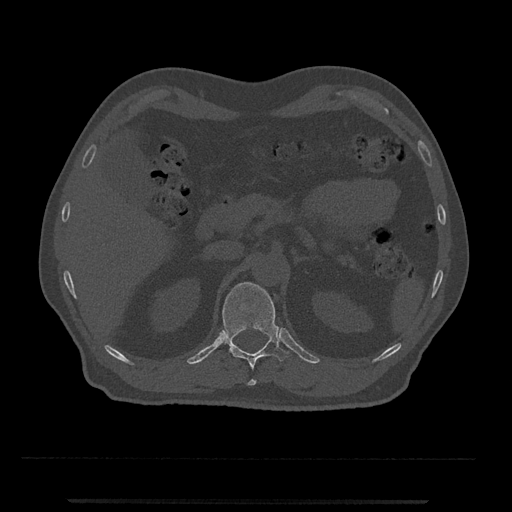
CT including the spine, one axial slice; reconstruction kernel Br40s/3; 120 kVp; bone window (W 1800 / L 400 HU); 0.5 mm slice thickness; 512 × 512 image matrix. Male patient, age 63 years. Case-level facts recorded for this patient, not image findings: primary cancer: prostate.
Structures marked on this image (semi-automatic segmentation, software-assisted and operator-edited):
- T12 vertebra: box from (x=221, y=282) to (x=289, y=386) px